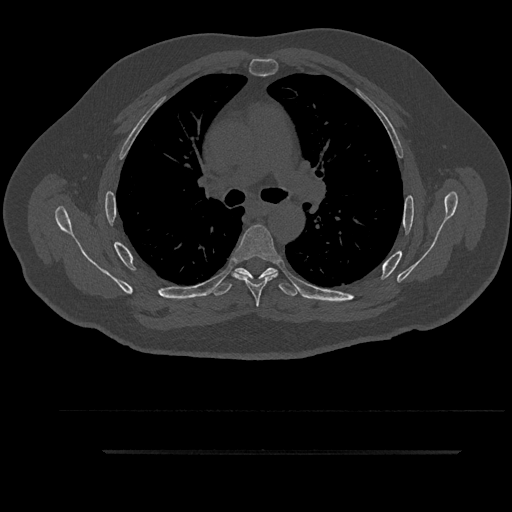
CT including the spine, one axial slice. Slice 612 of 797 in the series (ordered by position). 120 kVp. Bone window (W 1800 / L 400 HU). 512 × 512 image matrix. Patient: male, 63 years. Case-level facts recorded for this patient, not image findings: primary cancer: renal.
Outlined on this slice (semi-automatic segmentation, software-assisted and operator-edited):
- T5 vertebra: bounding box [x1, y1, x2, y2] px = [232, 225, 282, 307]
- T6 vertebra: [212, 268, 299, 296]